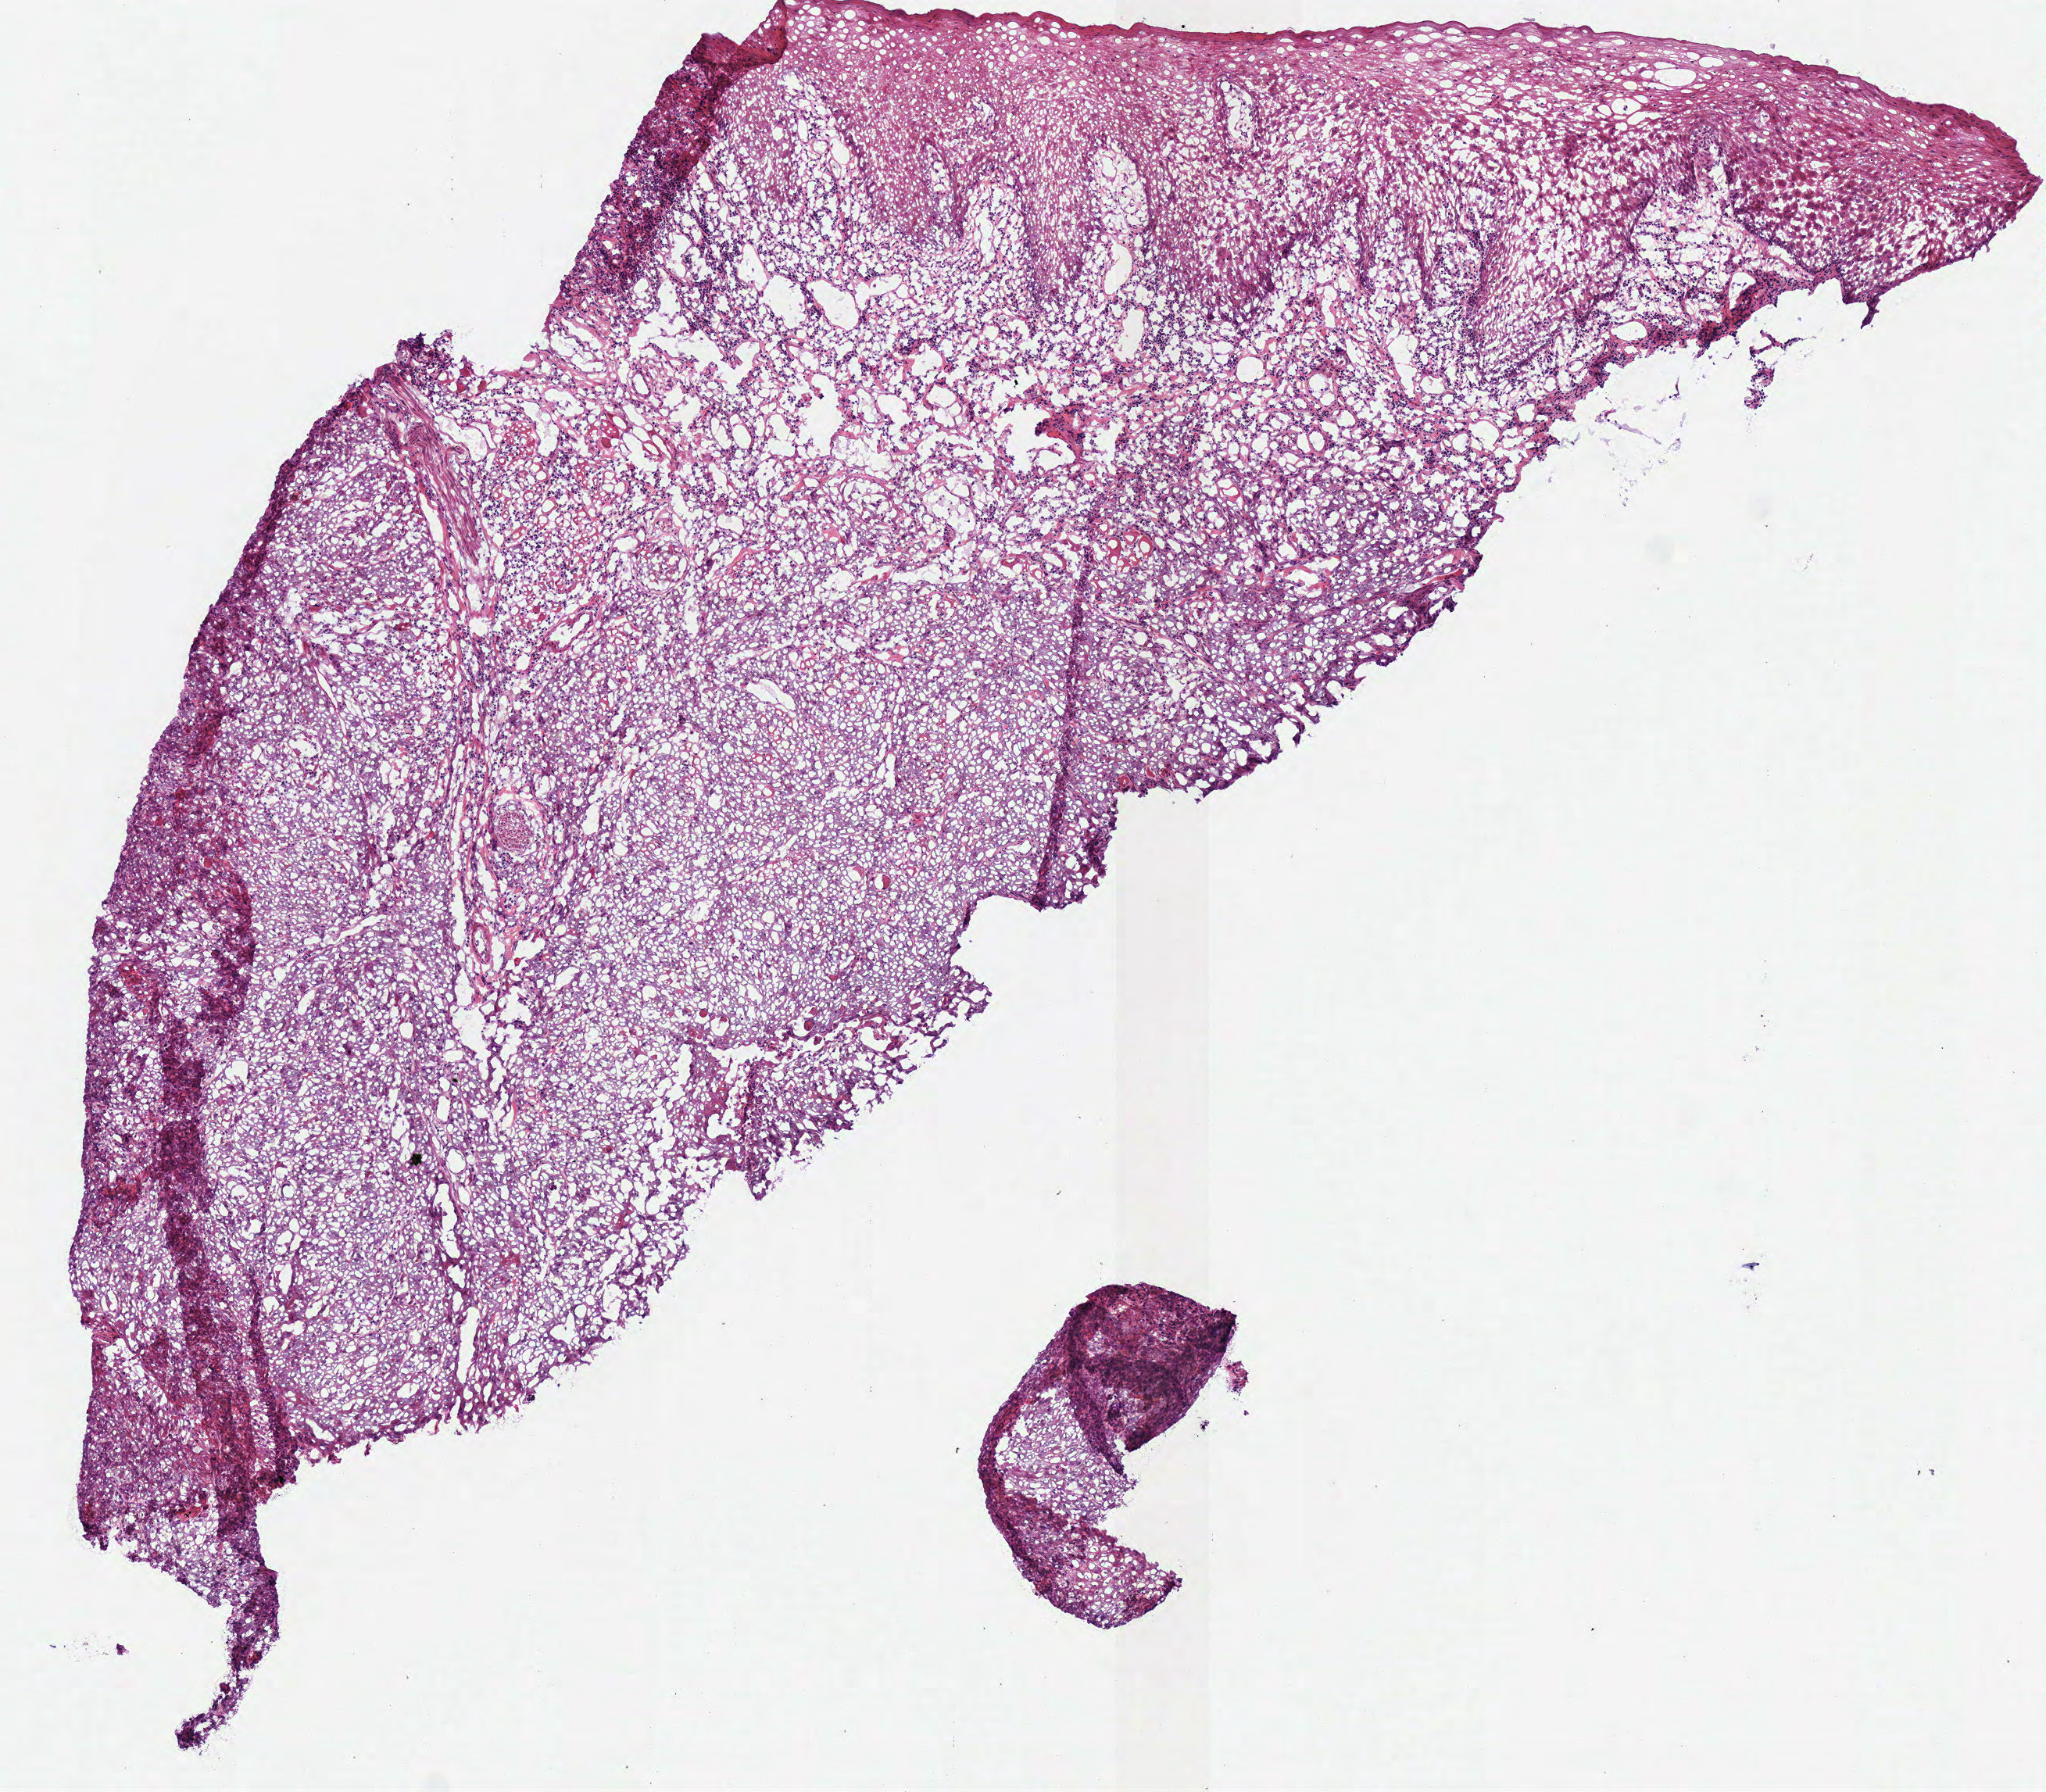
Digitized Hematoxylin and eosin (H&E) stained tissue section (whole slide), shown as a low-resolution overview of the whole scanned area (about 5.2 x 4.5 mm), frozen section from the top of the tissue portion, sample: primary tumour, head and neck. Patient: male, age at initial diagnosis 28 years. Histologic grade: G2 (moderately differentiated). Slide review estimates, as recorded: tumour cells 70%, tumour nuclei 80%, normal cells 18%, stromal cells 10%, necrosis 2%. Inflammatory infiltration, as recorded: lymphocyte infiltration 7%.
* AJCC pathologic stage: IVA (7th edition)
* histologic diagnosis: Squamous cell carcinoma, NOS
* laterality: left